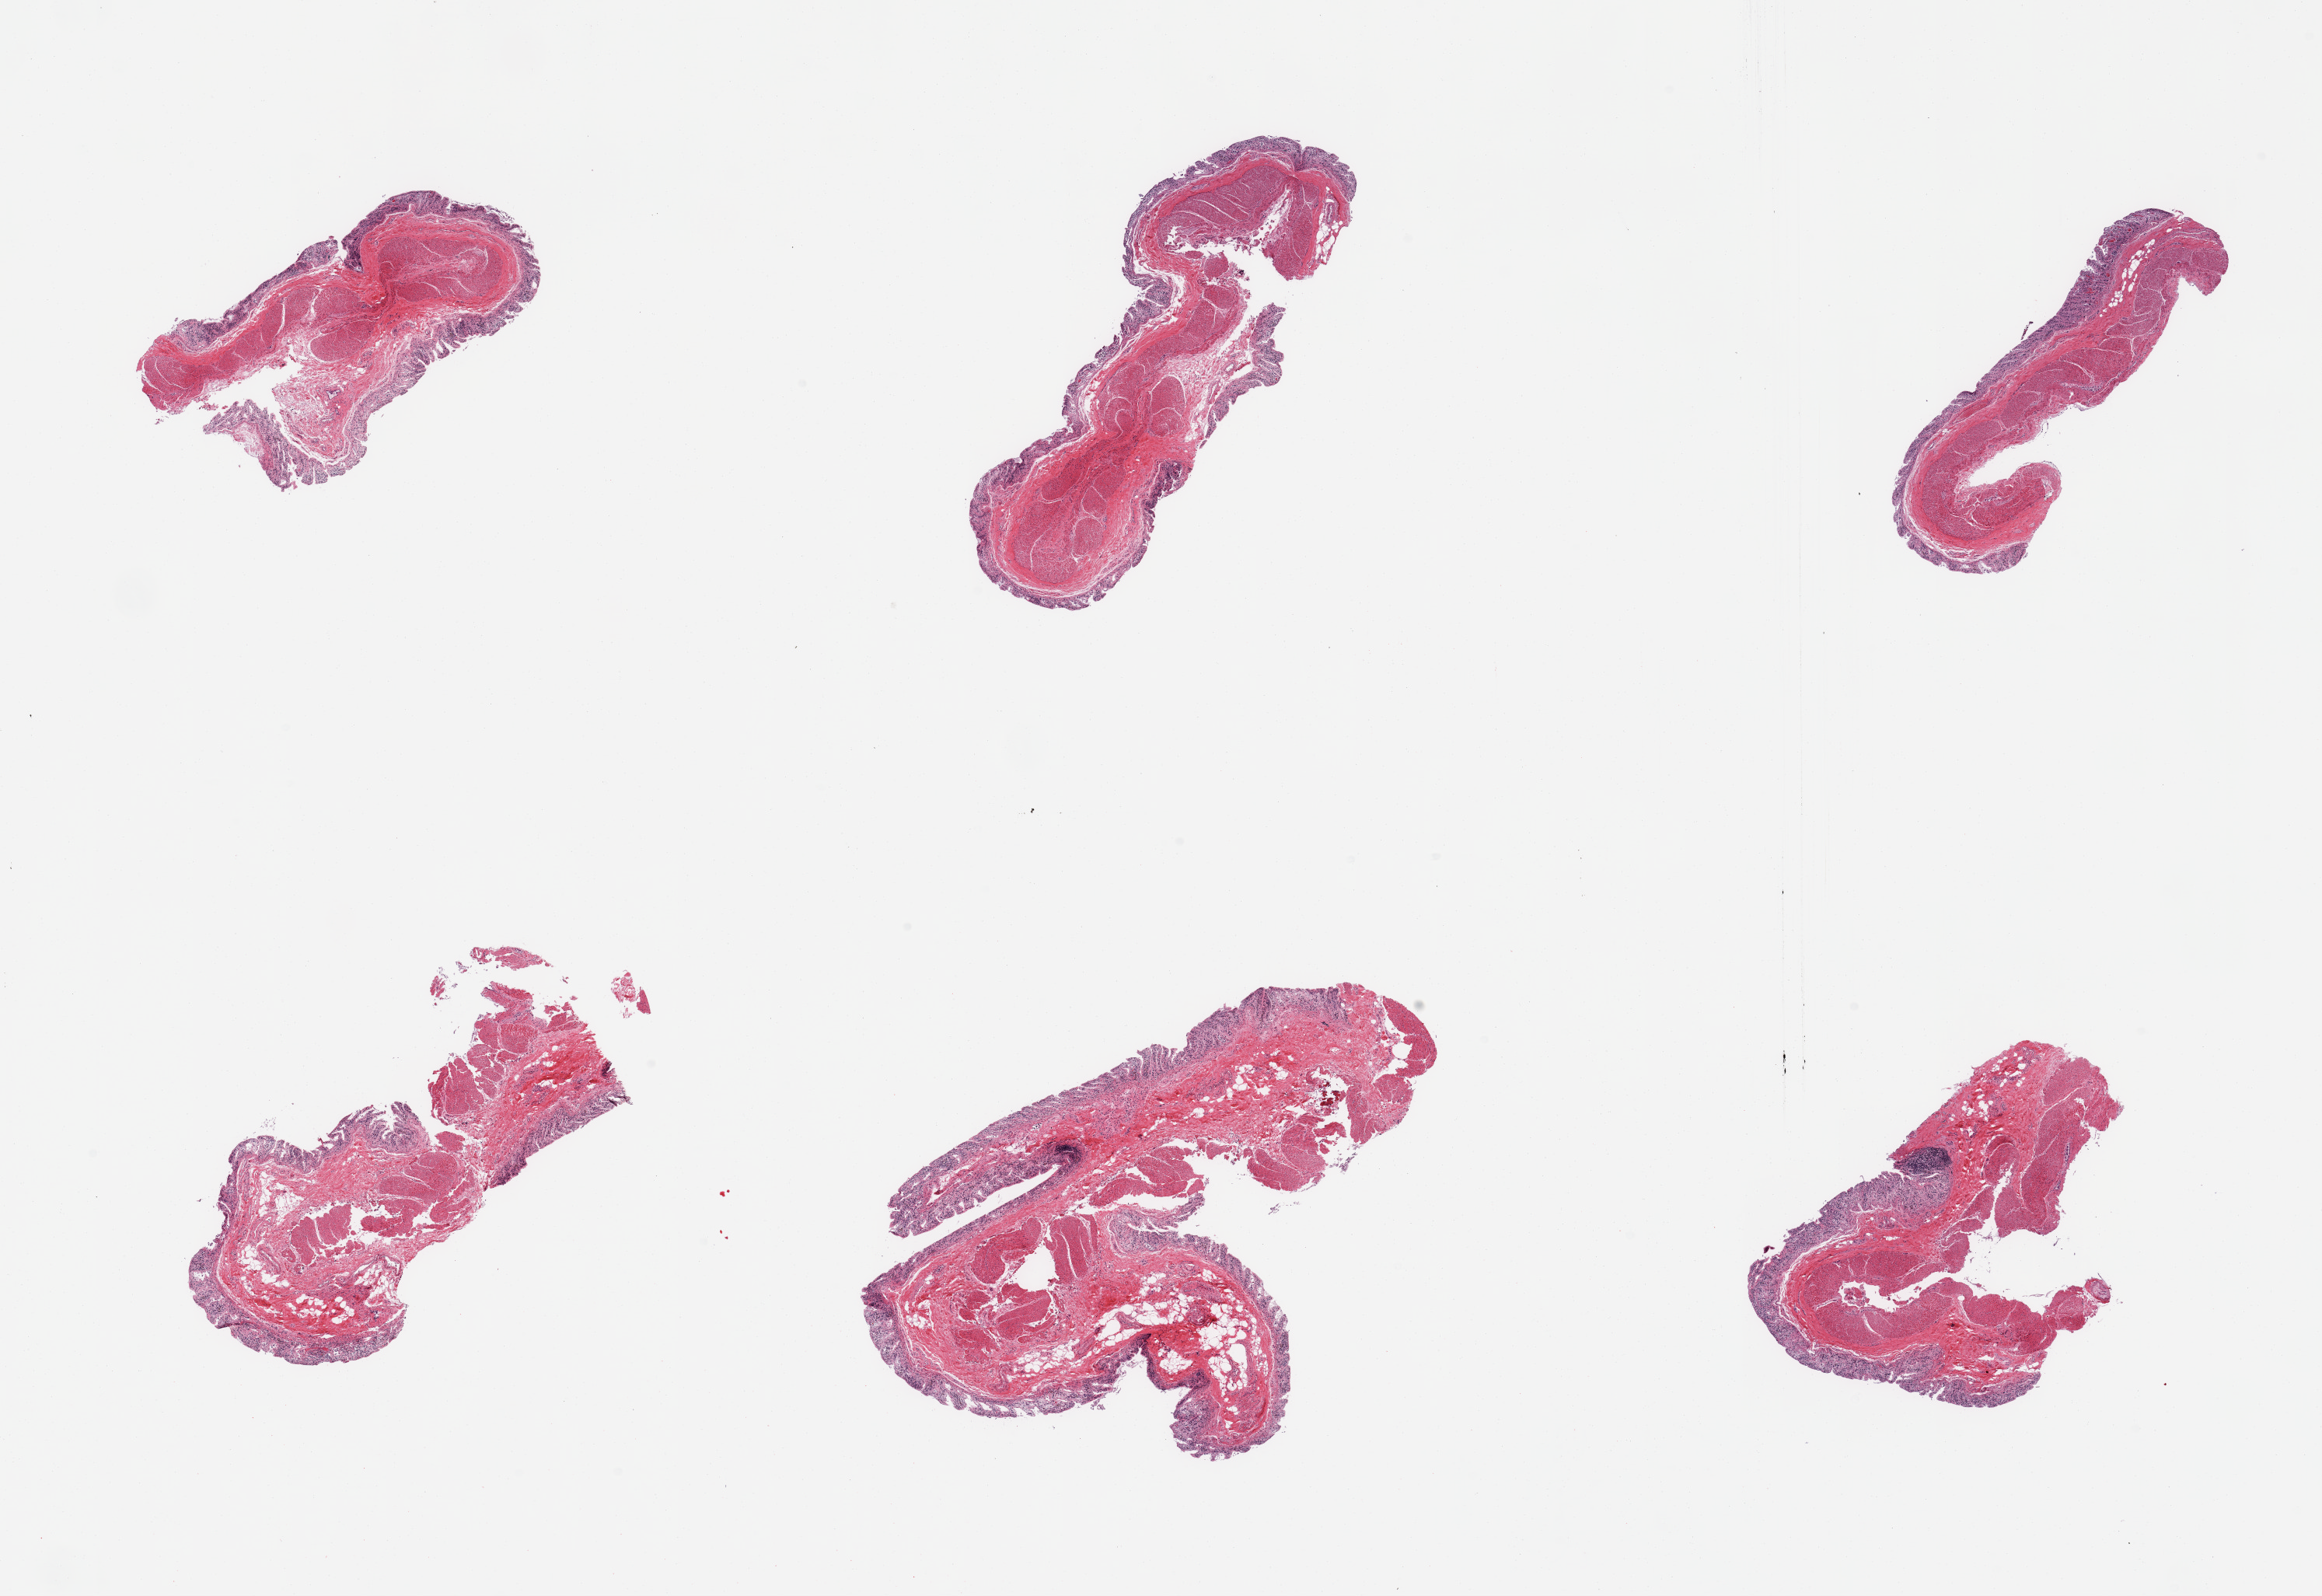
H&E whole-slide image, low-resolution overview of the scanned area, about 23.6 x 16.2 mm (from a 20x scan). PAXgene-fixed paraffin-embedded (PFPE) section. Target tissue: transverse colon. Tissue donor sample. Donor sex: female.
- pathologist's review note for this sample: 6 pieces; glands totally autolyzed, remainder of wall intact